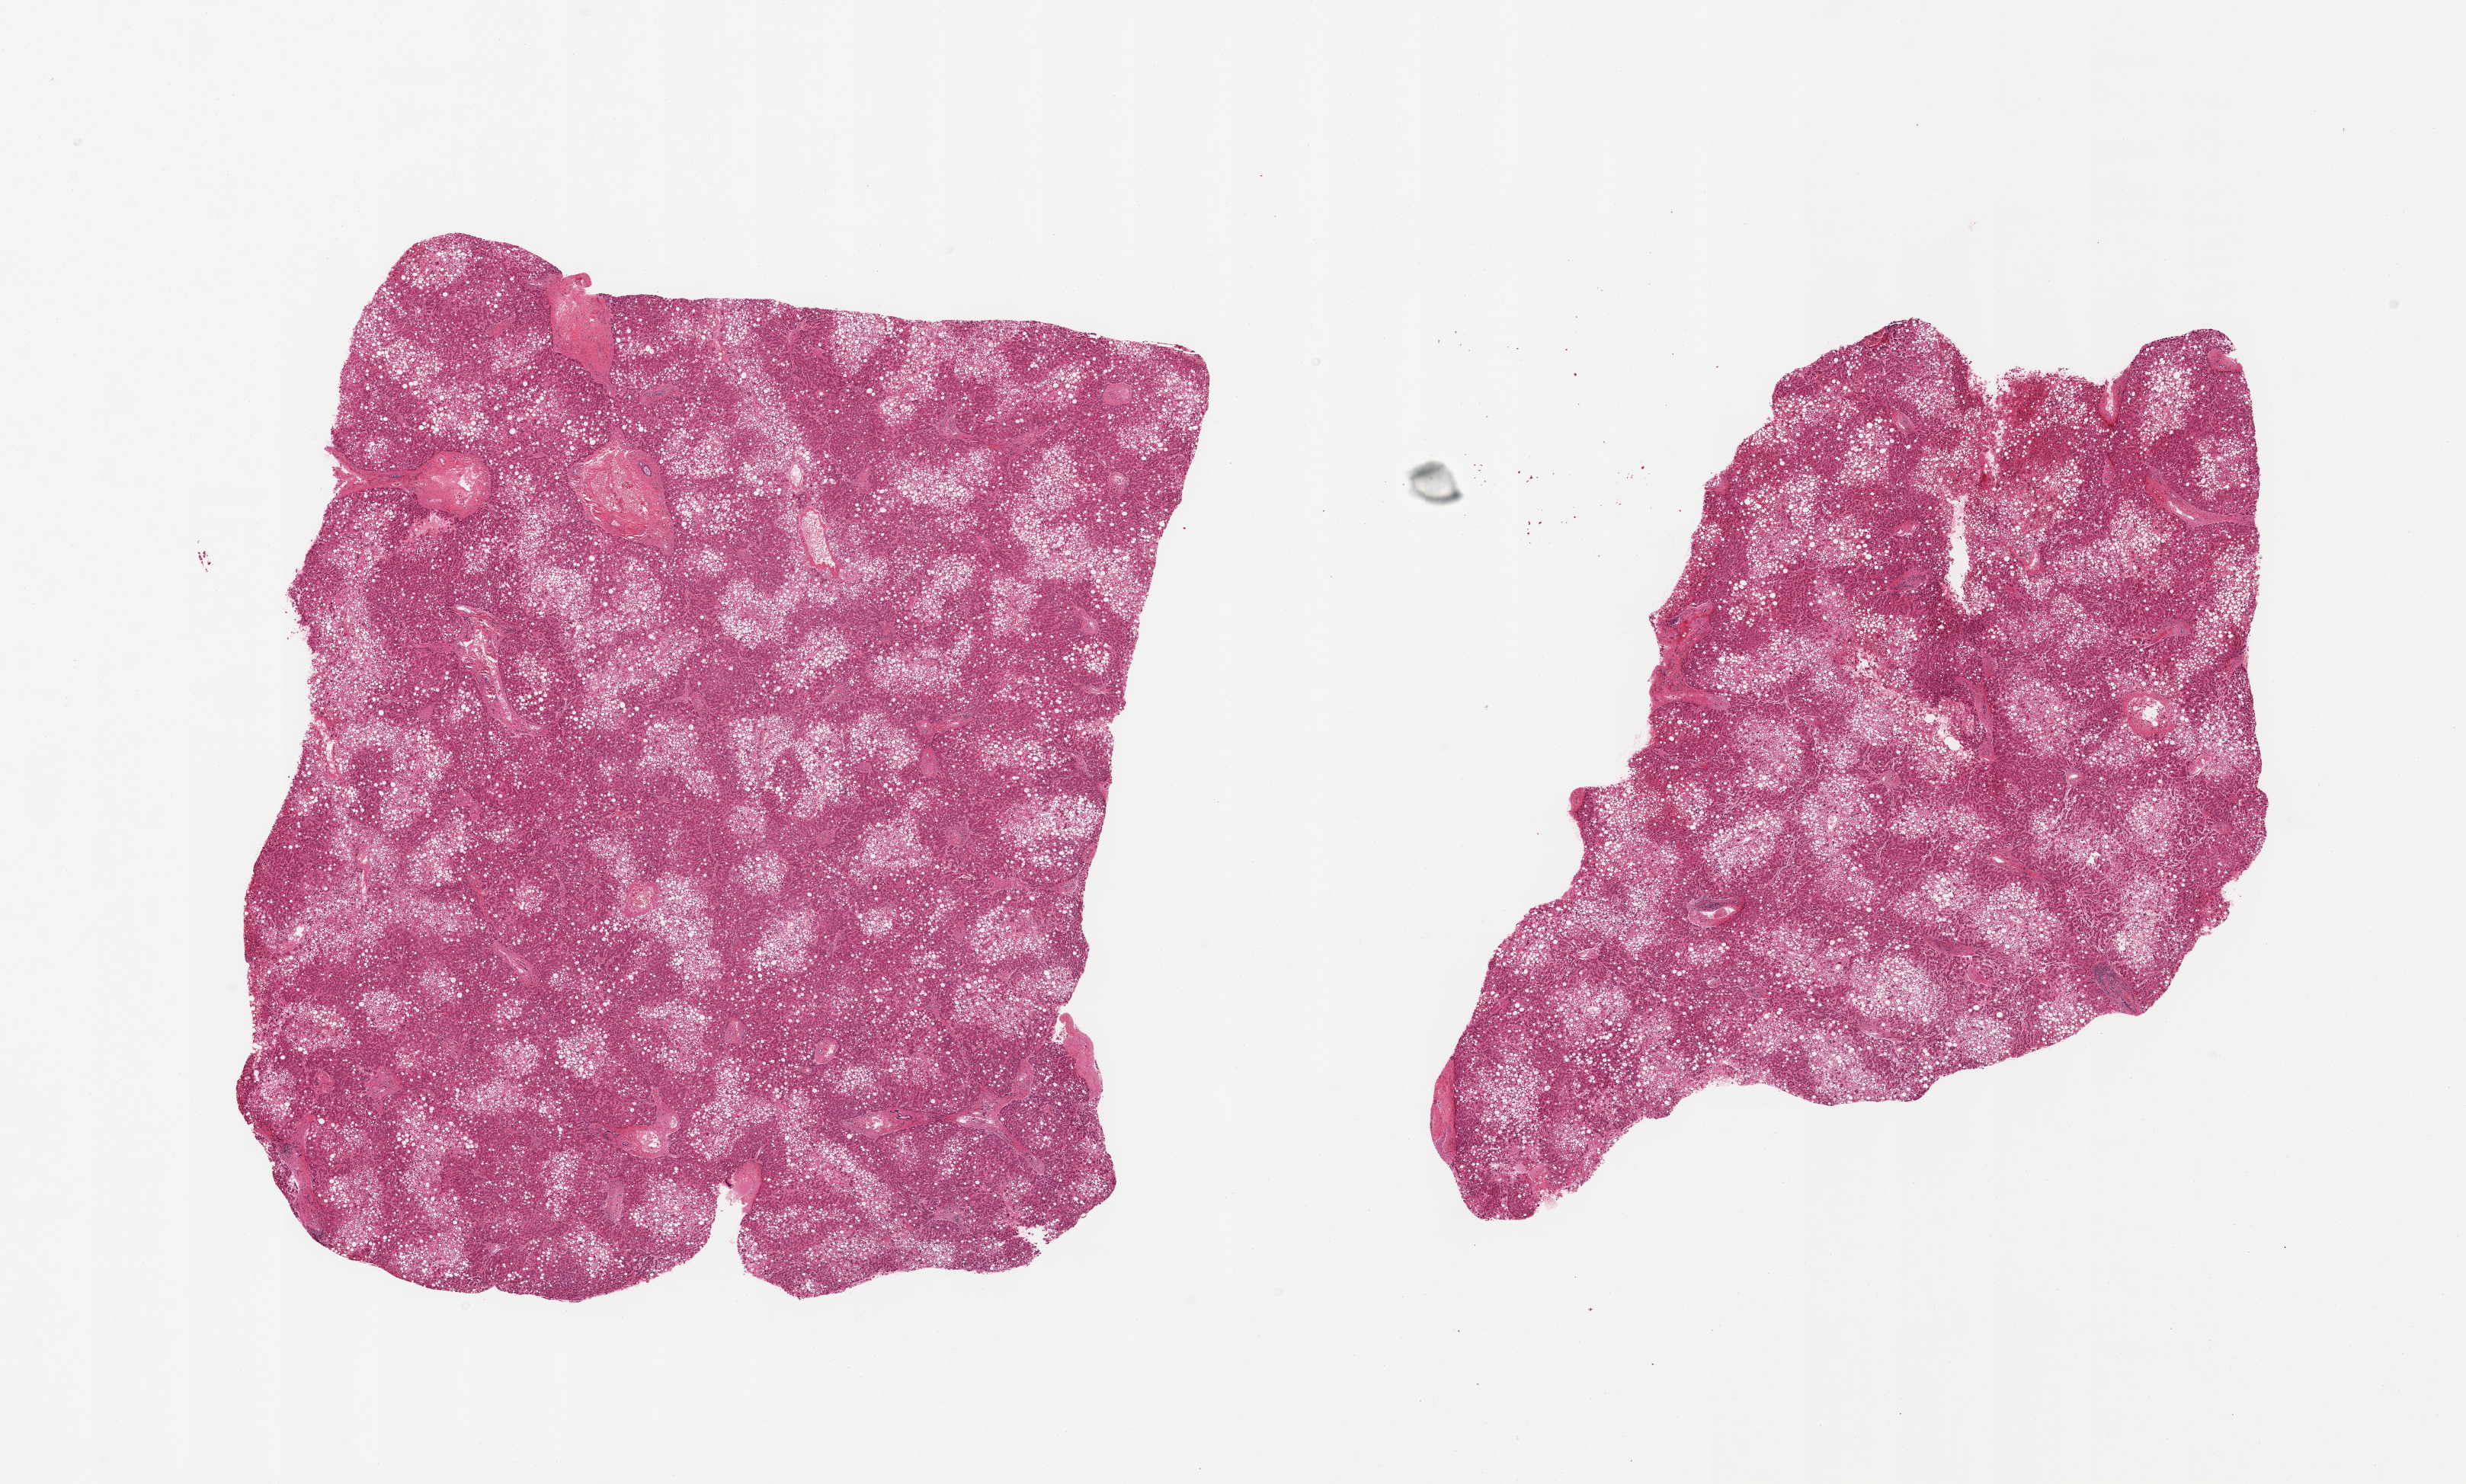
Digitized hematoxylin and eosin (H&E)-stained section — shown as a low-resolution overview of the whole scanned area (about 25.6 x 15.4 mm, acquisition: 20x scan). PAXgene-fixed paraffin-embedded (PFPE) section. Section of liver (target tissue). Donor tissue sample. Donor: male.
- reviewer comment on this tissue sample: 2 pieces, macrovesicular steatosis, moderate